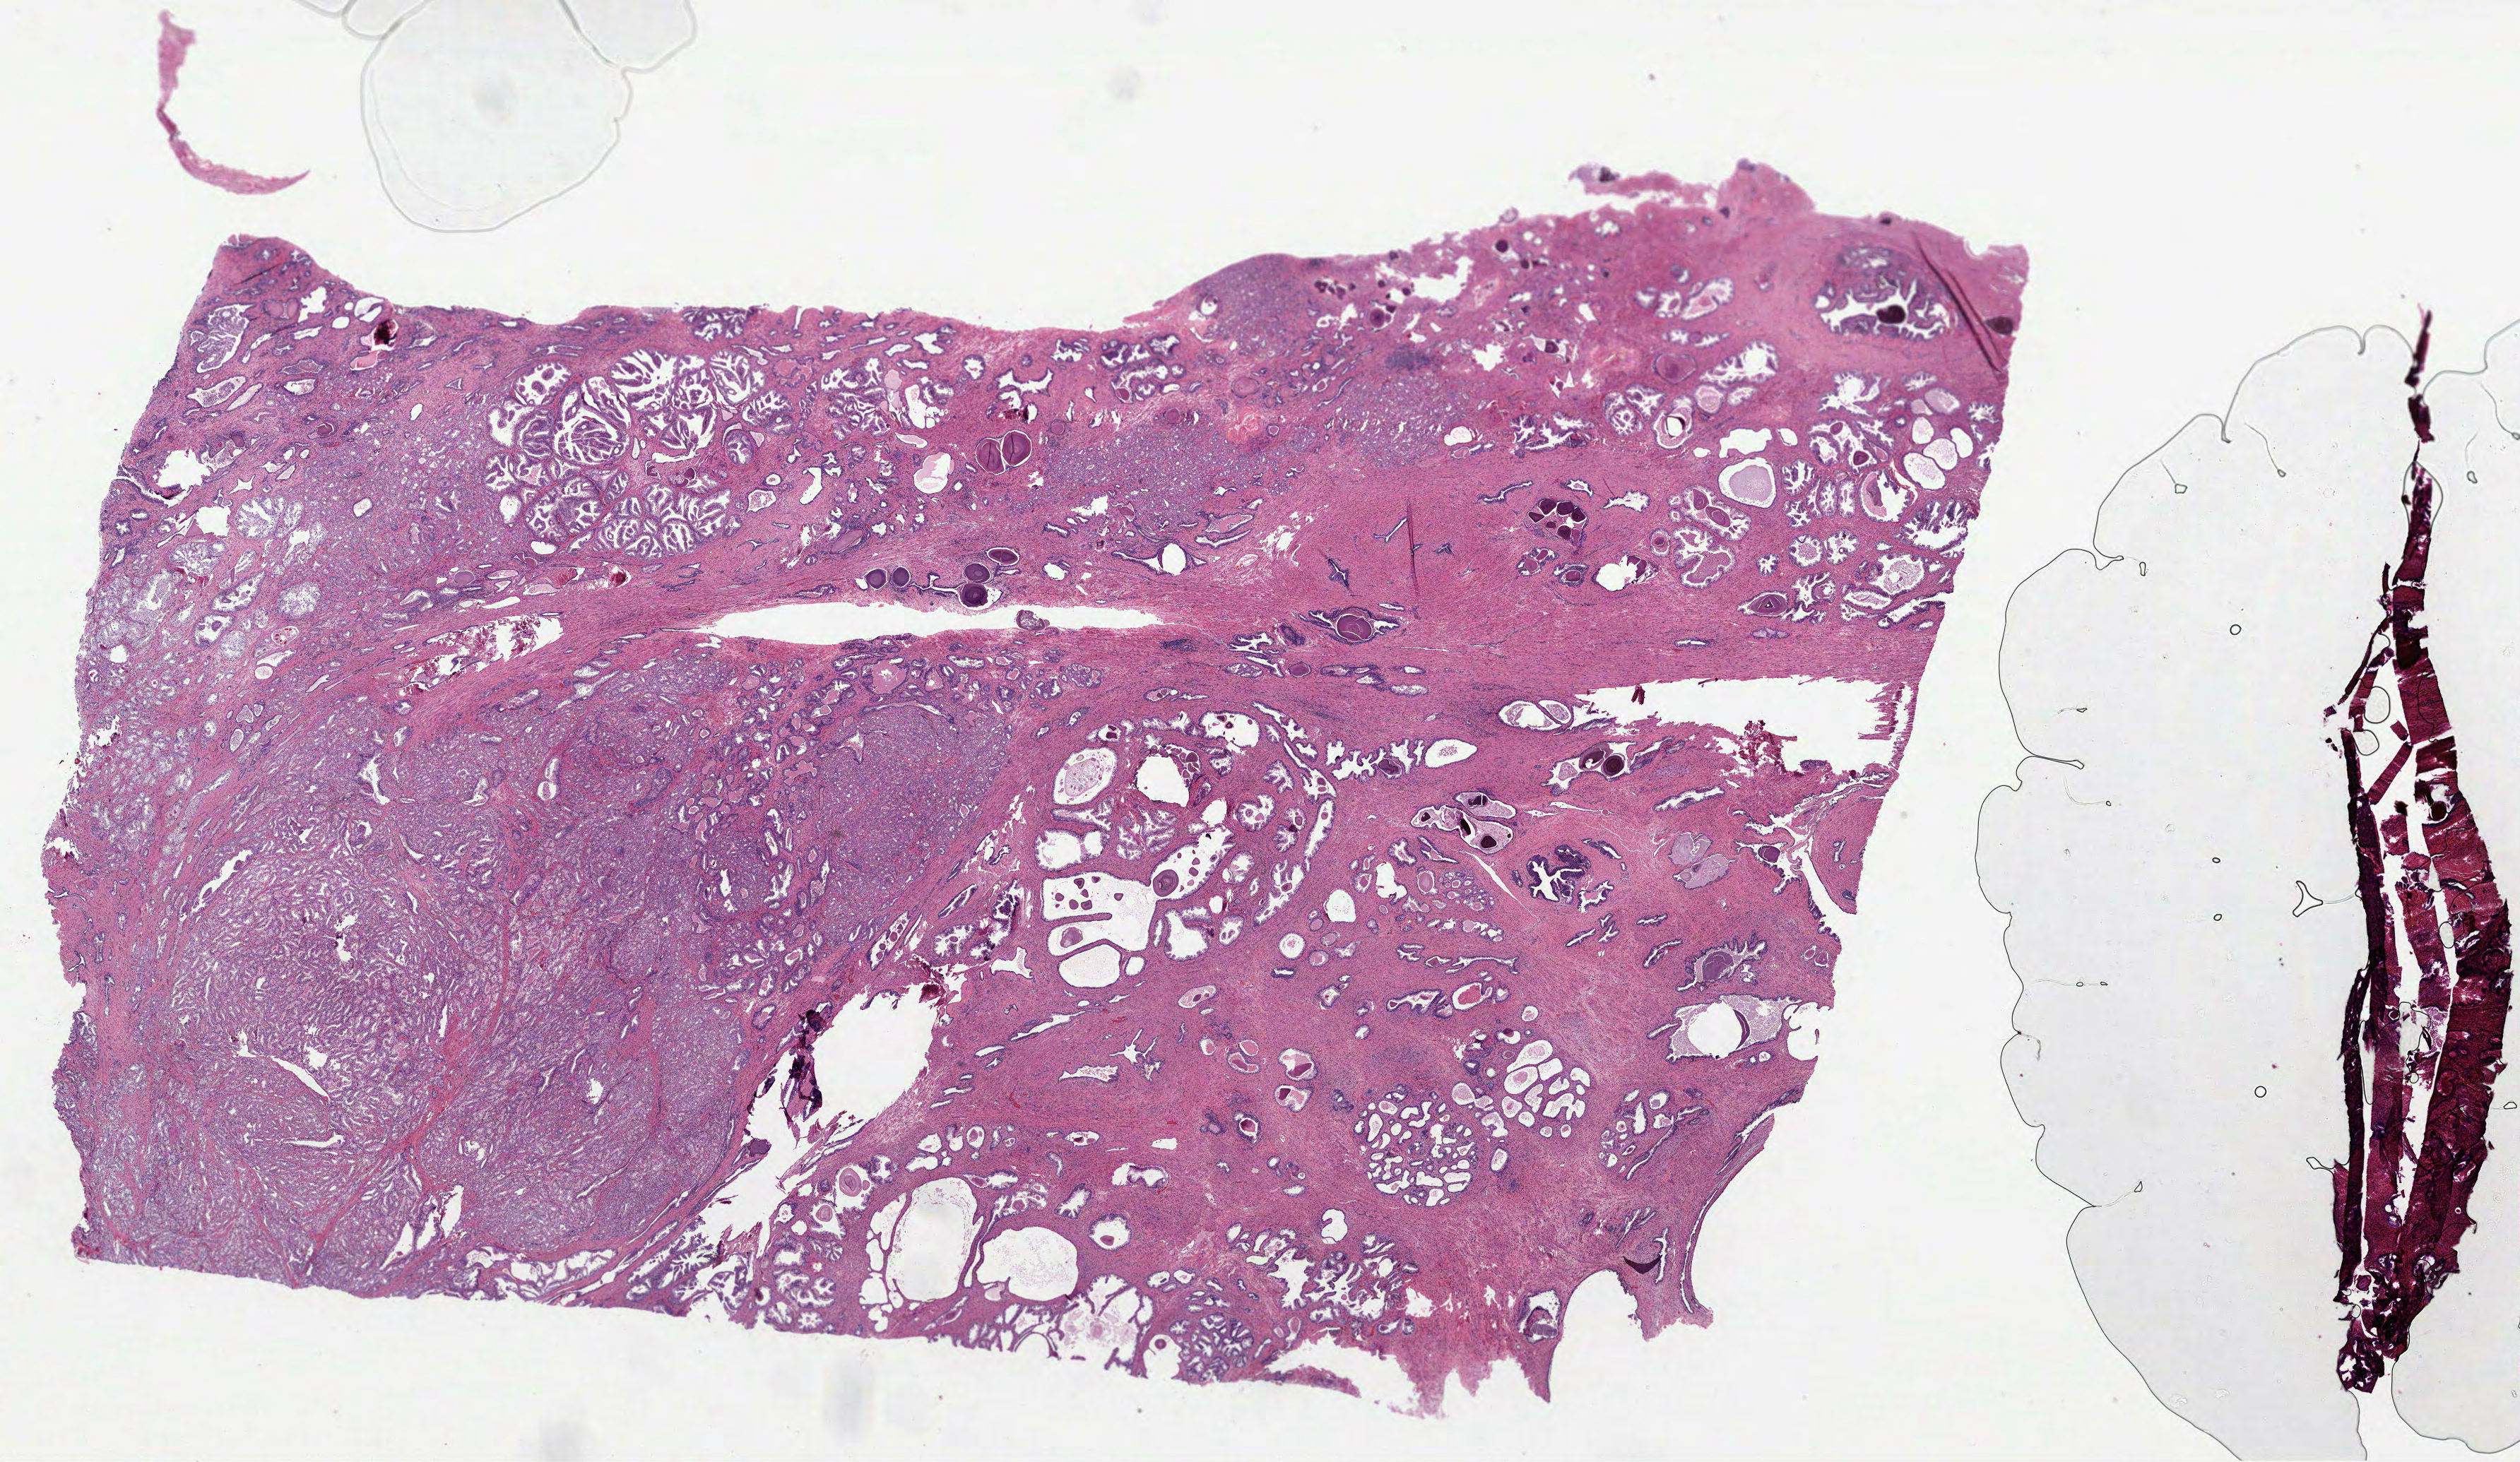
Digitized H&E tissue section (whole slide), a low-resolution overview of the entire scanned area, about 28.8 x 16.7 mm (acquisition: 40x scan). Formalin-fixed paraffin-embedded (FFPE) diagnostic section. Sample: primary tumour, prostate. Male, age 68 years at initial diagnosis. Gleason score: 7 (4+3).
Histologic diagnosis: Acinar cell carcinoma (prostate gland). Lymph nodes positive (case pathology): 0 of 18 examined. Laterality: bilateral.